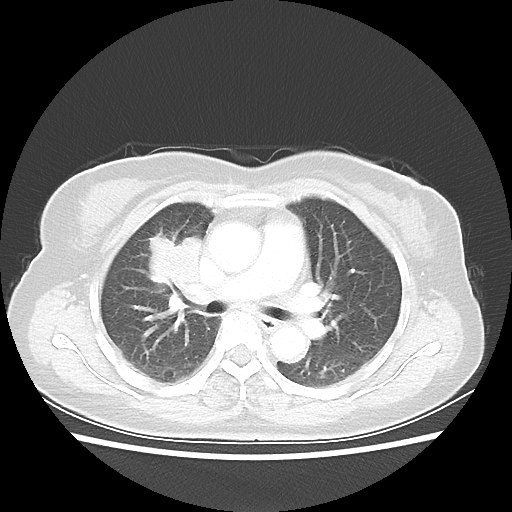
Chest CT, one axial slice; position 33 of 55 along the scan axis; lung window (W 1500 / L -600 HU); 5 mm slice thickness; 512 × 512 image matrix, field of view 337 × 337 mm. Female patient, age 62 years. Case-level facts recorded for this patient, not image findings: clinical TNM (as recorded): T4 N3 M0.
Outlined on this slice (bounding box drawn by a radiologist):
- lung tumour (recorded histology: squamous cell carcinoma): bounding box <139,230,211,305> (left, top, right, bottom; pixels)